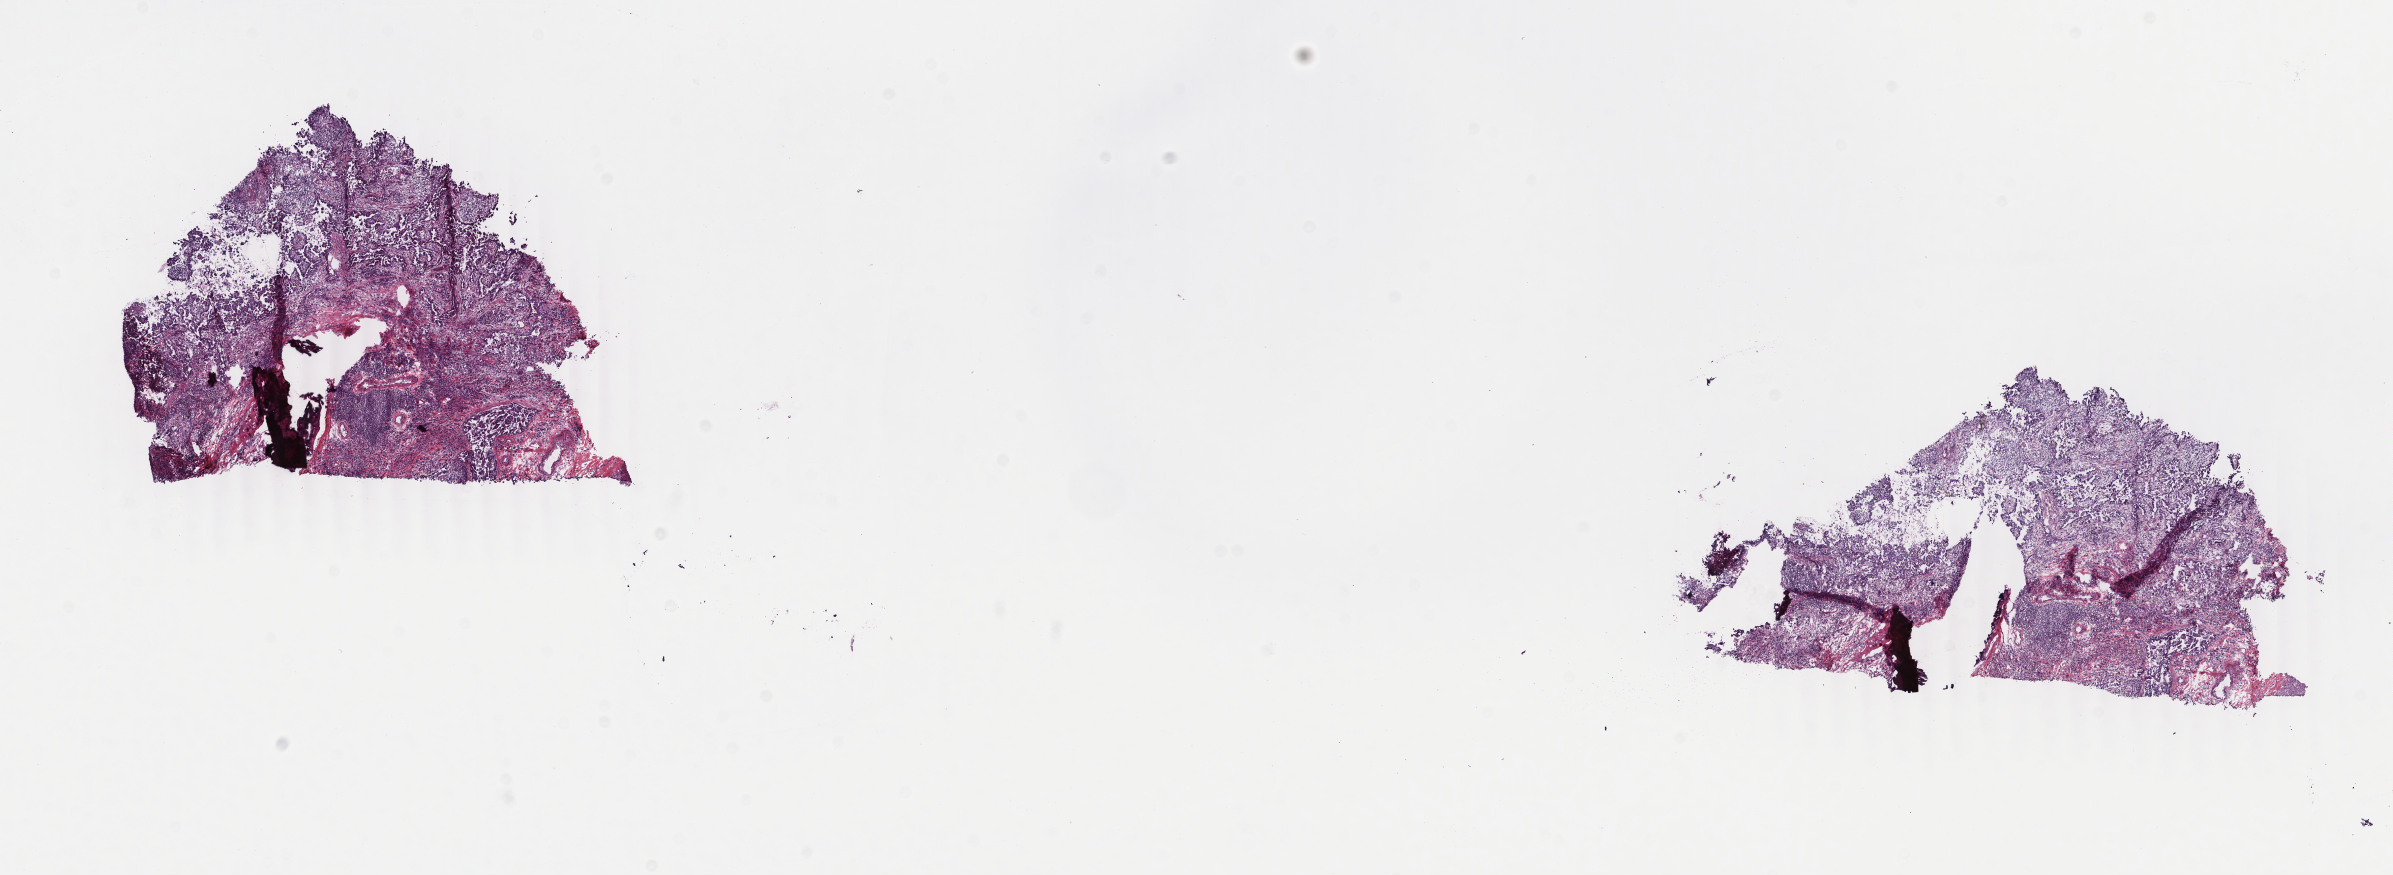
Whole-slide histology image, H&E, a low-resolution overview of the entire scanned area, about 19.0 x 7.0 mm, frozen section from the top of the tissue portion, primary tumour sample from the lung. Male patient; age at initial diagnosis 71 years. Pathologist review of this section (percent, as recorded): tumour cells 80%, tumour nuclei 80%, normal cells 0%, stromal cells 20%, necrosis 0%. Infiltration values recorded for this section: lymphocyte infiltration 4%, monocyte infiltration 2%, neutrophil infiltration 2%.
AJCC pathologic stage: IV. TNM: T2a N0 M1a. Laterality: left. Pathologic diagnosis: Acinar cell carcinoma (upper lobe, lung).